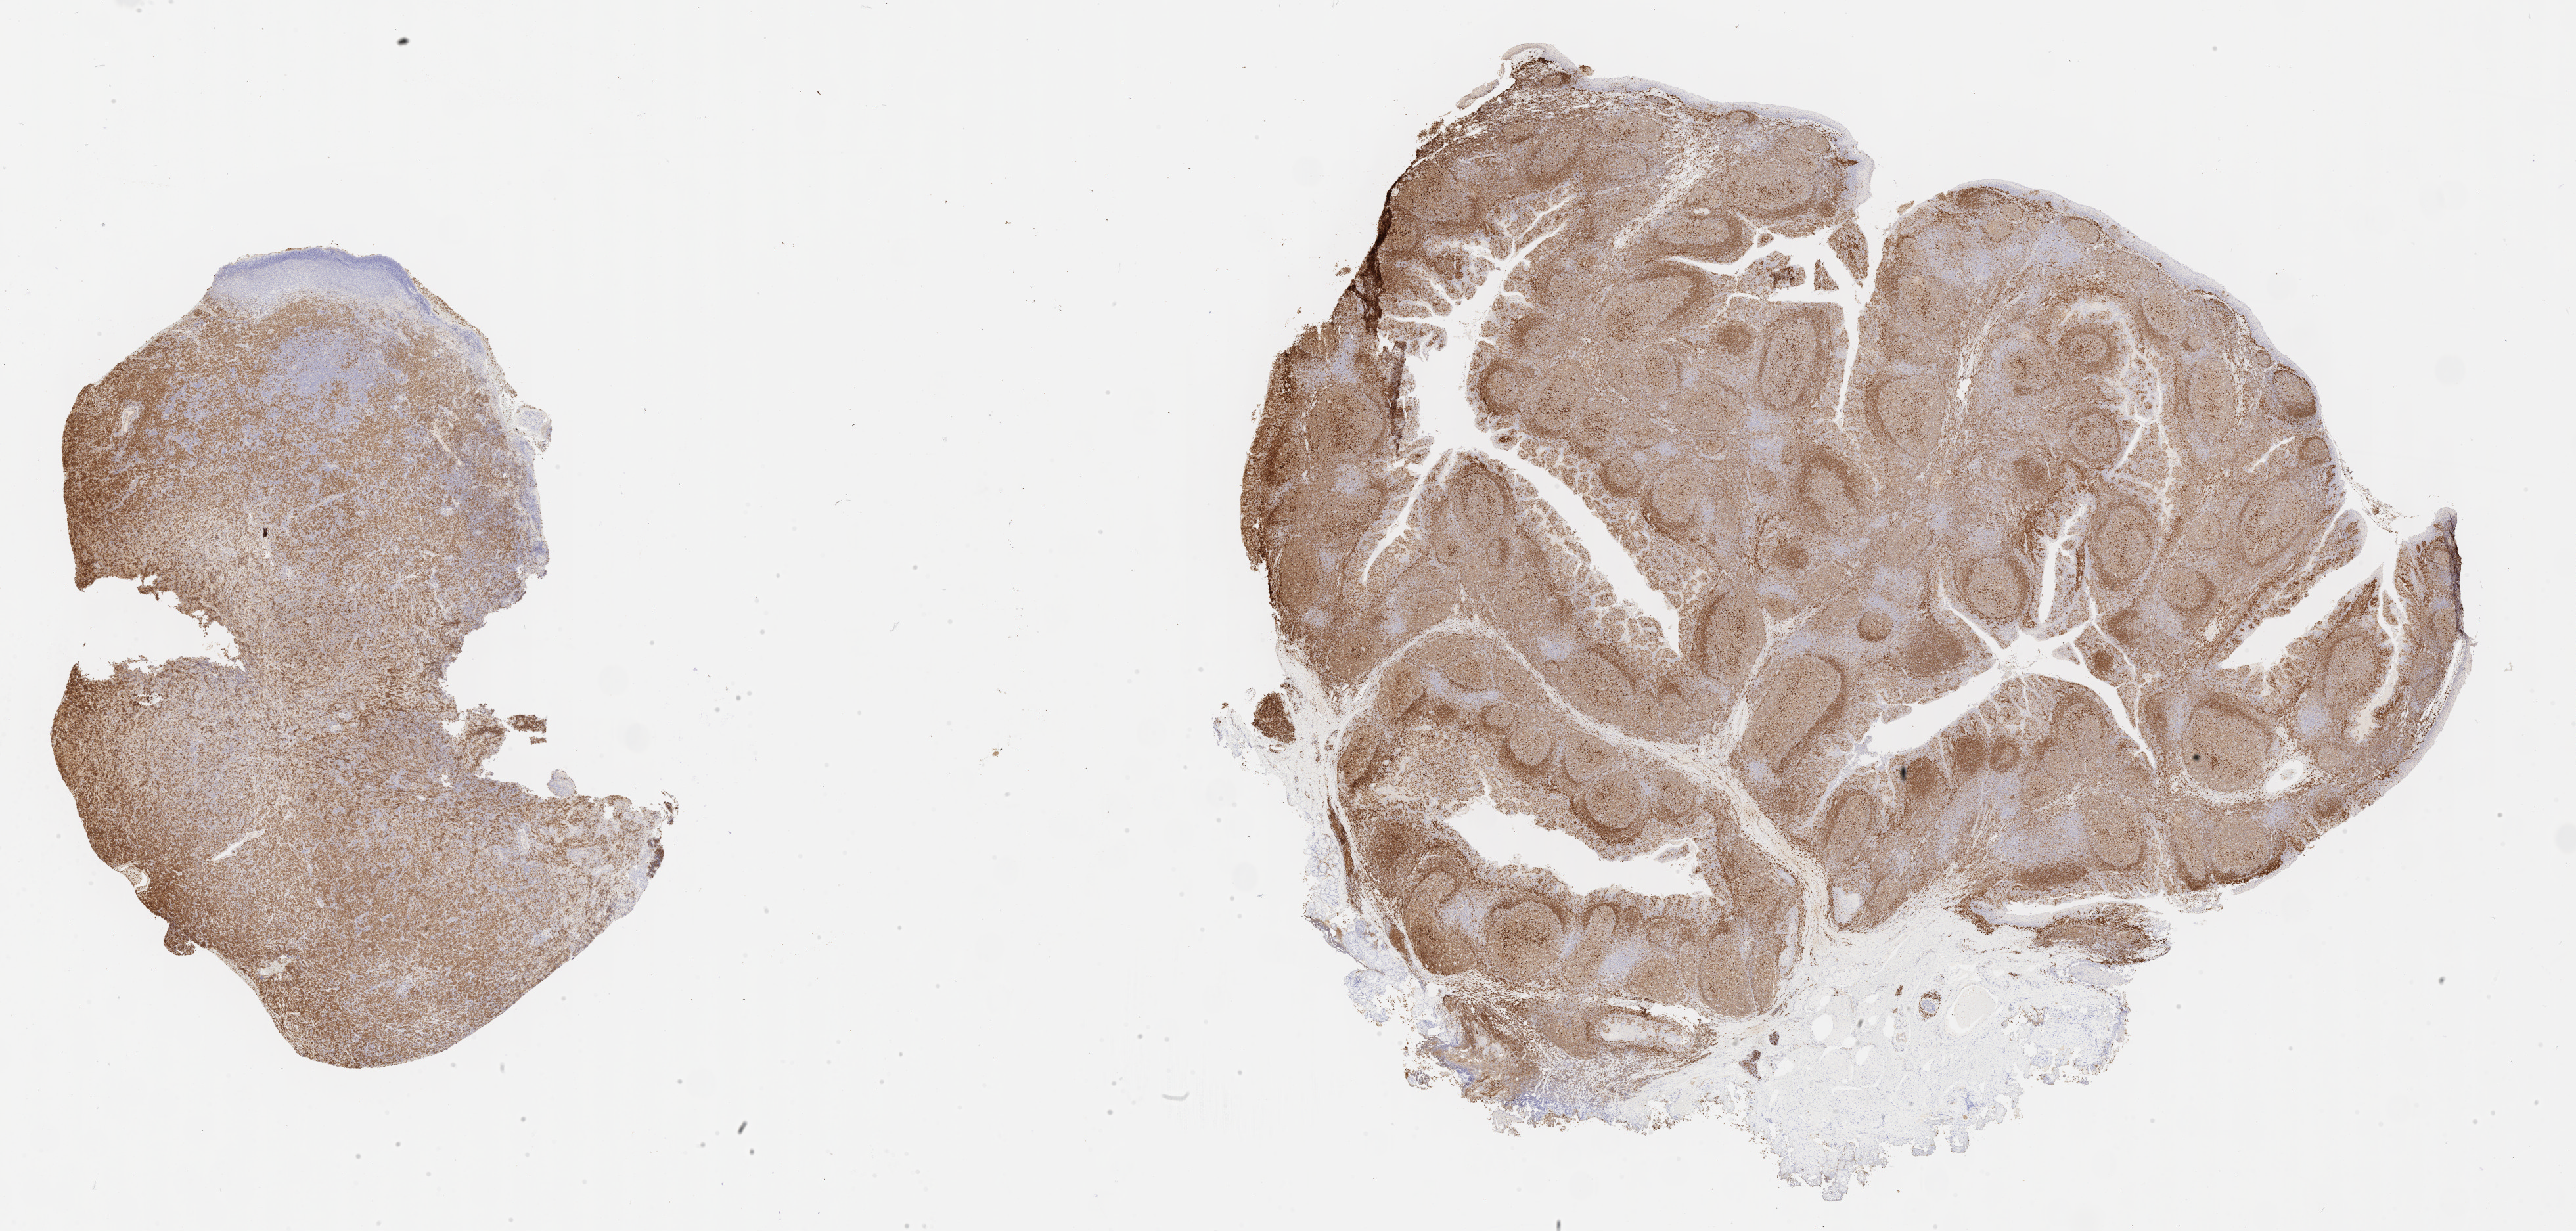
Immunohistochemistry (IHC) whole-slide image stained for CD79a, low-resolution overview of the scanned area, about 31.7 x 15.2 mm, specimen: tumor tissue. Male, age 7 years at initial diagnosis.
Histologic diagnosis: Diffuse large B-cell lymphoma, NOS.